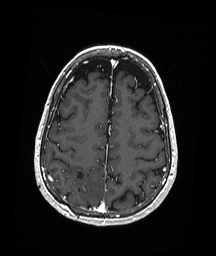
Brain MRI from a brain-tumour surgery series, one axial slice; slice 67 of 192 in the series (ordered by position); T1-weighted post-contrast; 1 mm slice thickness; 216 × 256 image matrix, field of view 211 × 250 mm. From the clinical record (not read from this slice): histopathology: Astrocytoma; WHO grade: 3; IDH mutation: yes.
Outlined on this slice (manually delineated by an expert):
- previous resection cavity: bounding box <78,172,83,190> (left, top, right, bottom; pixels)